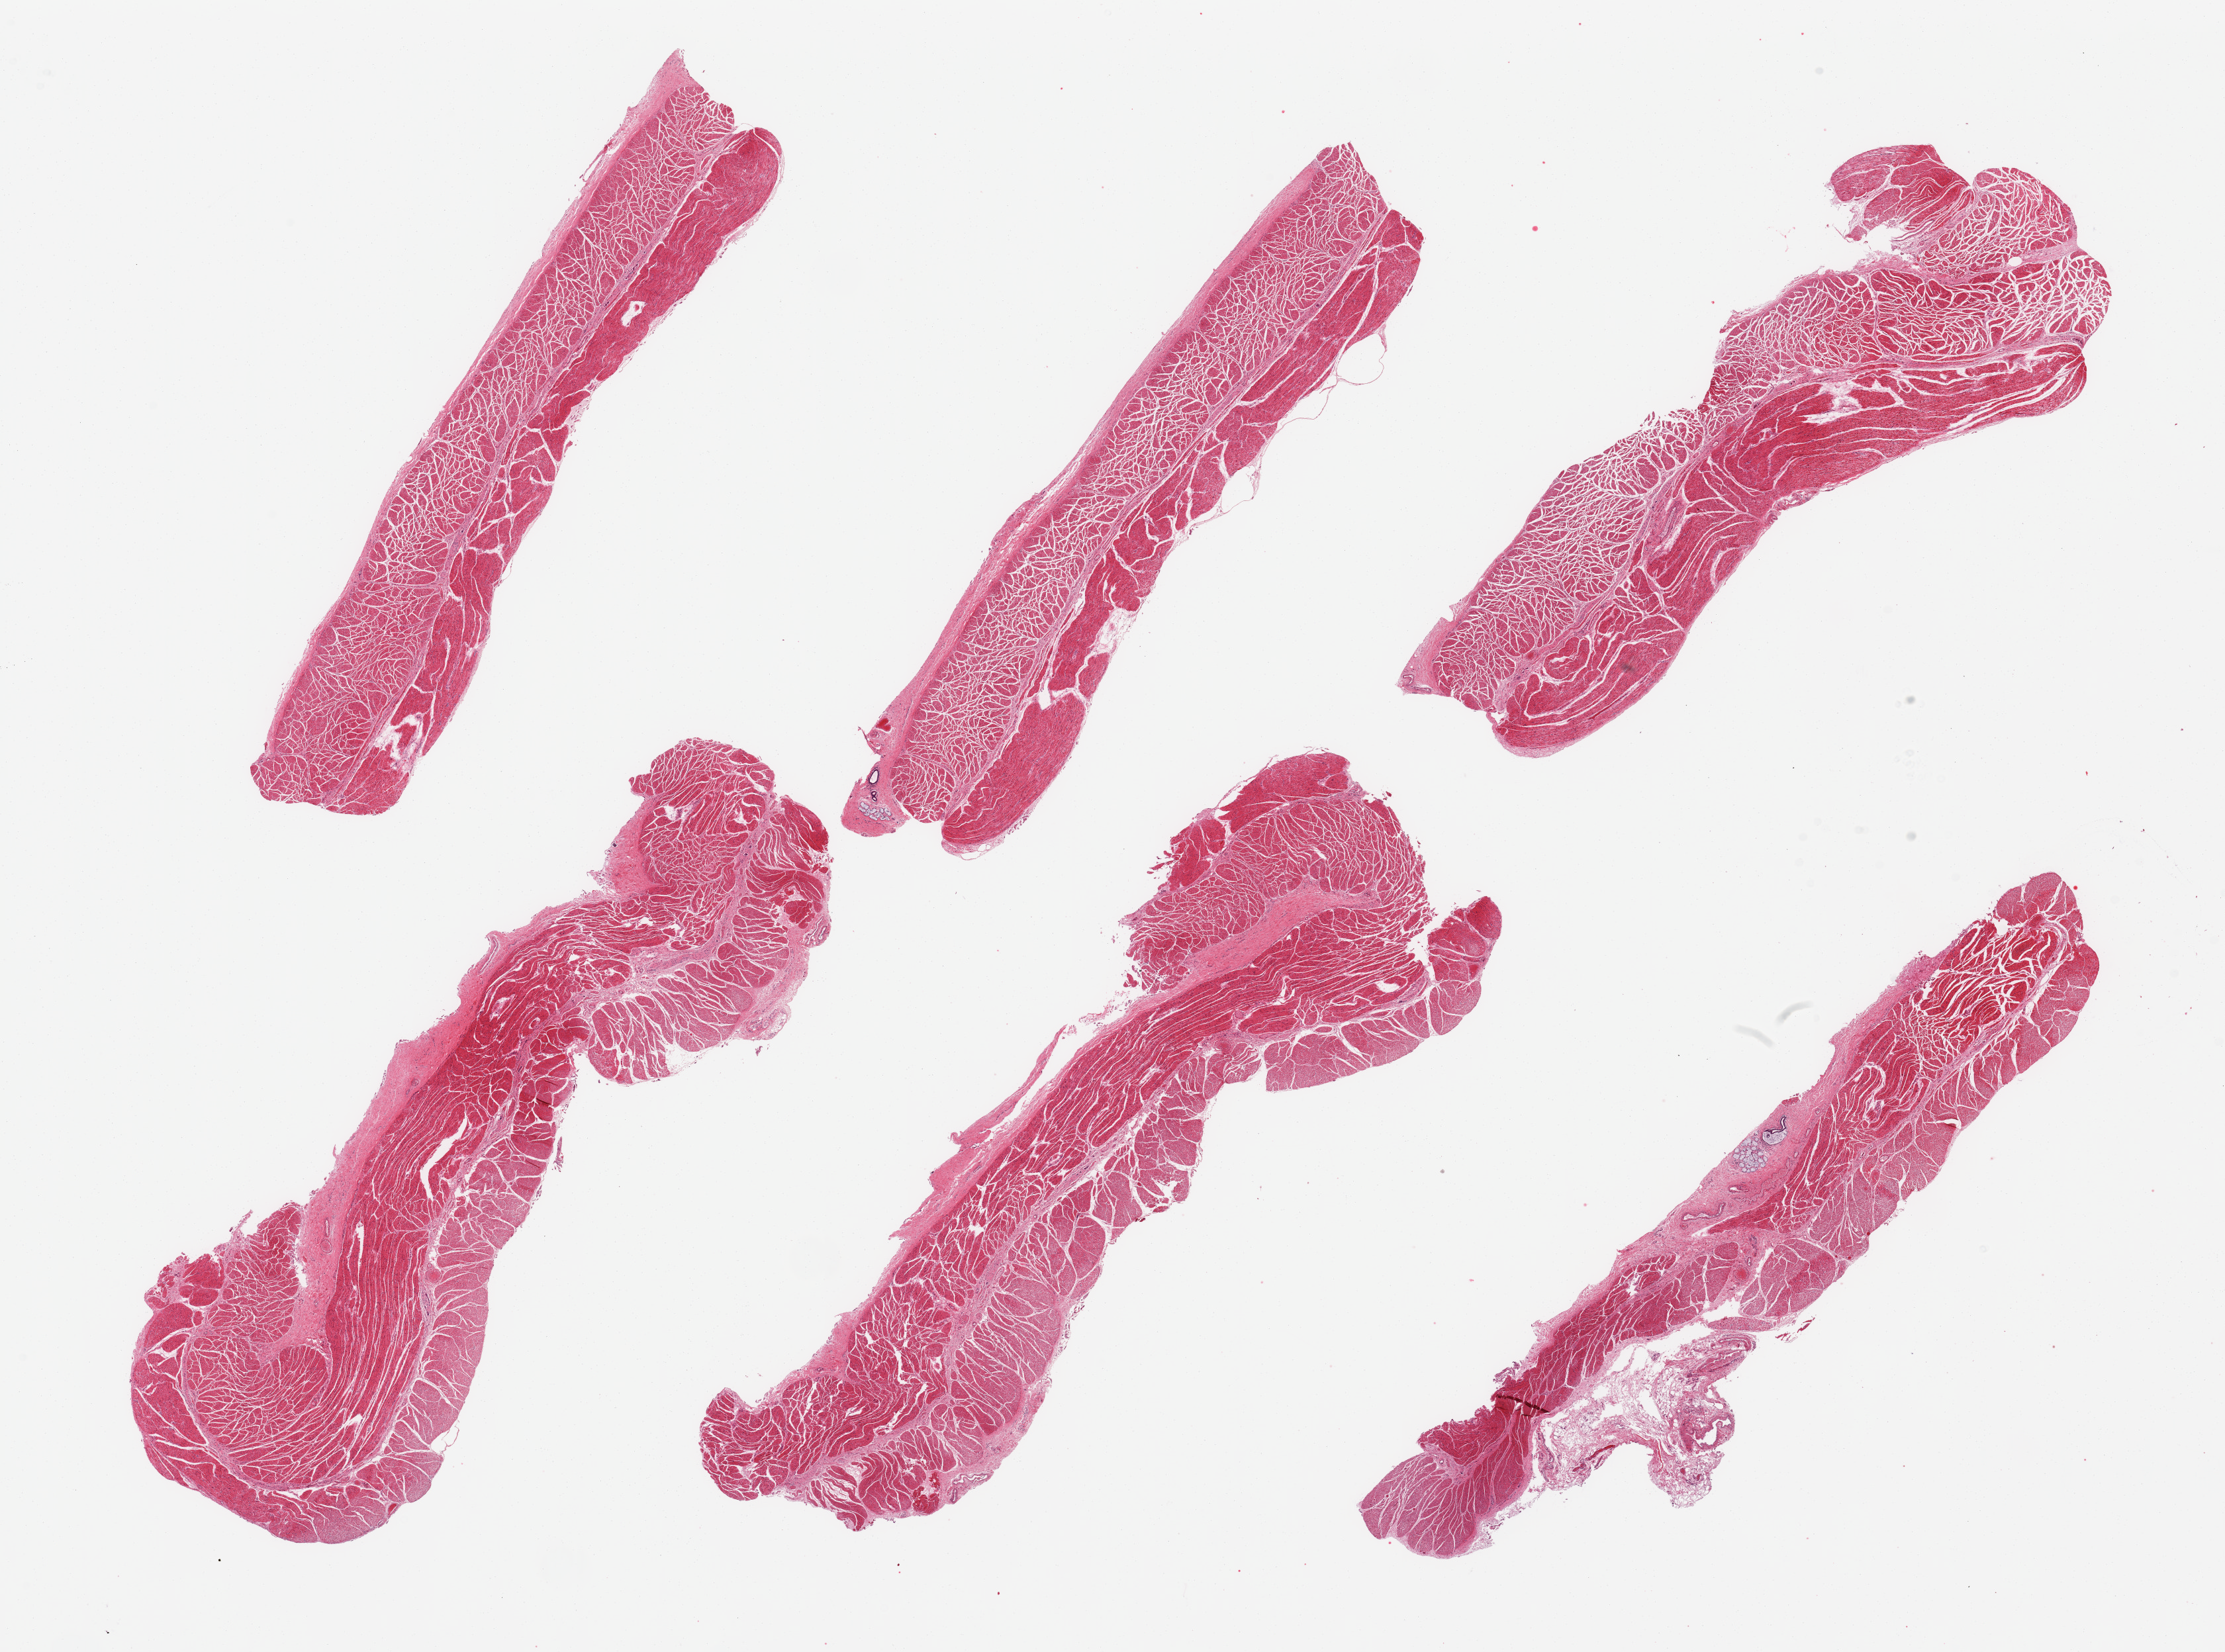
Whole-slide image, H&E stain — a low-resolution overview of the entire scanned area, about 26.6 x 19.7 mm (acquisition: 20x scan). PAXgene-fixed, paraffin-embedded tissue. Target tissue: esophageal muscle. Donor tissue sample. Male donor.
- reviewer comment on this tissue sample: 6 pieces, confirmed target muscularis